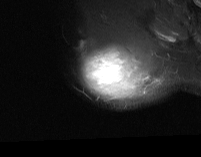
MRI of an extremity soft-tissue mass, one axial slice; position 57 of 74 along the scan axis; STIR; MR volume resampled by the dataset authors to the PET/CT grid (not the native acquisition matrix); 3.27 mm slice thickness; 201 × 157 image matrix, field of view 196 × 153 mm. Male patient. Case-level facts recorded for this patient, not image findings: histological type: pleiomorphic spindle cell undifferentiated; grade: high; site of the primary tumour: right parascapusular.
Annotated regions visible in this slice (expert contour drawn on MRI and transferred to this co-registered scan by the dataset authors):
- gross tumour volume including surrounding oedema: bounding box <81,52,155,95> (left, top, right, bottom; pixels)
- gross tumour volume (mass): <85,52,134,92>